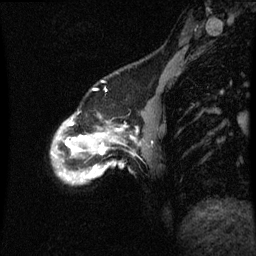
Breast MRI (dynamic contrast-enhanced), one sagittal slice; slice 12 of 60 in the series (ordered by position); dynamic contrast-enhanced series, image 2 of 3 at this slice position (ordered by acquisition); 1.5 T; TE 4.2 ms, TR 8.9 ms; 2 mm slice thickness; 256 × 256 image matrix. Patient: female, 49 years. Case-level facts recorded for this patient, not image findings: setting: breast cancer imaged before/during neoadjuvant chemotherapy; receptor status: HR-positive, HER2-negative.
Outlined on this slice (semi-automatically segmented with operator editing):
- analysis volume of interest (the breast-tissue region the enhancement analysis was run in; not a lesion): bounding box <52,114,143,185> (left, top, right, bottom; pixels)
- tumour enhancement mask (voxels above the 70 % enhancement threshold inside the analysis volume of interest): <74,138,105,171>